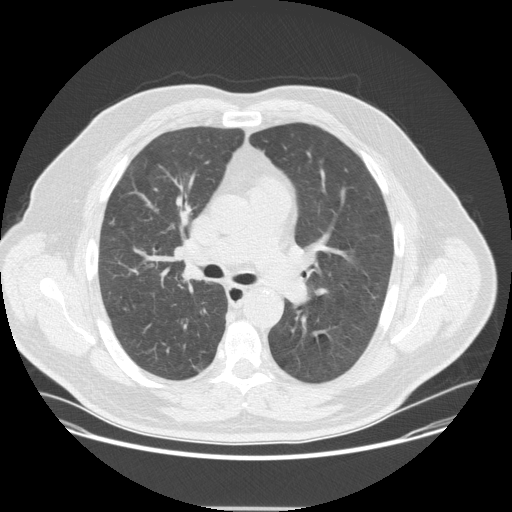
Low-dose screening chest CT, one axial slice; slice 219 of 351 in the series (ordered by position); 120 kVp; lung window (W 1500 / L -600 HU); 512 × 512 image matrix.
Outlined on this slice (manually delineated by an expert):
- lesion 1 (tumor, upper lobe of right lung): box from (x=182, y=273) to (x=196, y=282) px